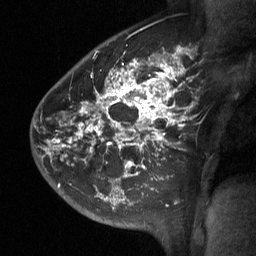
Breast MRI (dynamic contrast-enhanced), one sagittal slice; position 45 of 64 along the scan axis; dynamic contrast-enhanced study with each time point stored as its own series, time point 2 of 3 at this slice position (early post-contrast, ordered by acquisition time); 1.5 T; TE 4.8 ms, TR 27 ms; 2 mm slice thickness; 256 × 256 image matrix, field of view 200 × 200 mm. Female patient, age 42 years. Case-level facts recorded for this patient, not image findings: setting: breast cancer imaged before/during neoadjuvant chemotherapy; receptor status: triple-negative.
Structures marked on this image (semi-automatically segmented with operator editing):
- analysis volume of interest (the breast-tissue region the enhancement analysis was run in; not a lesion): box from (x=49, y=45) to (x=195, y=197) px
- tumour enhancement mask (voxels above the 90 % enhancement threshold inside the analysis volume of interest): (x=49, y=47)–(x=186, y=177)